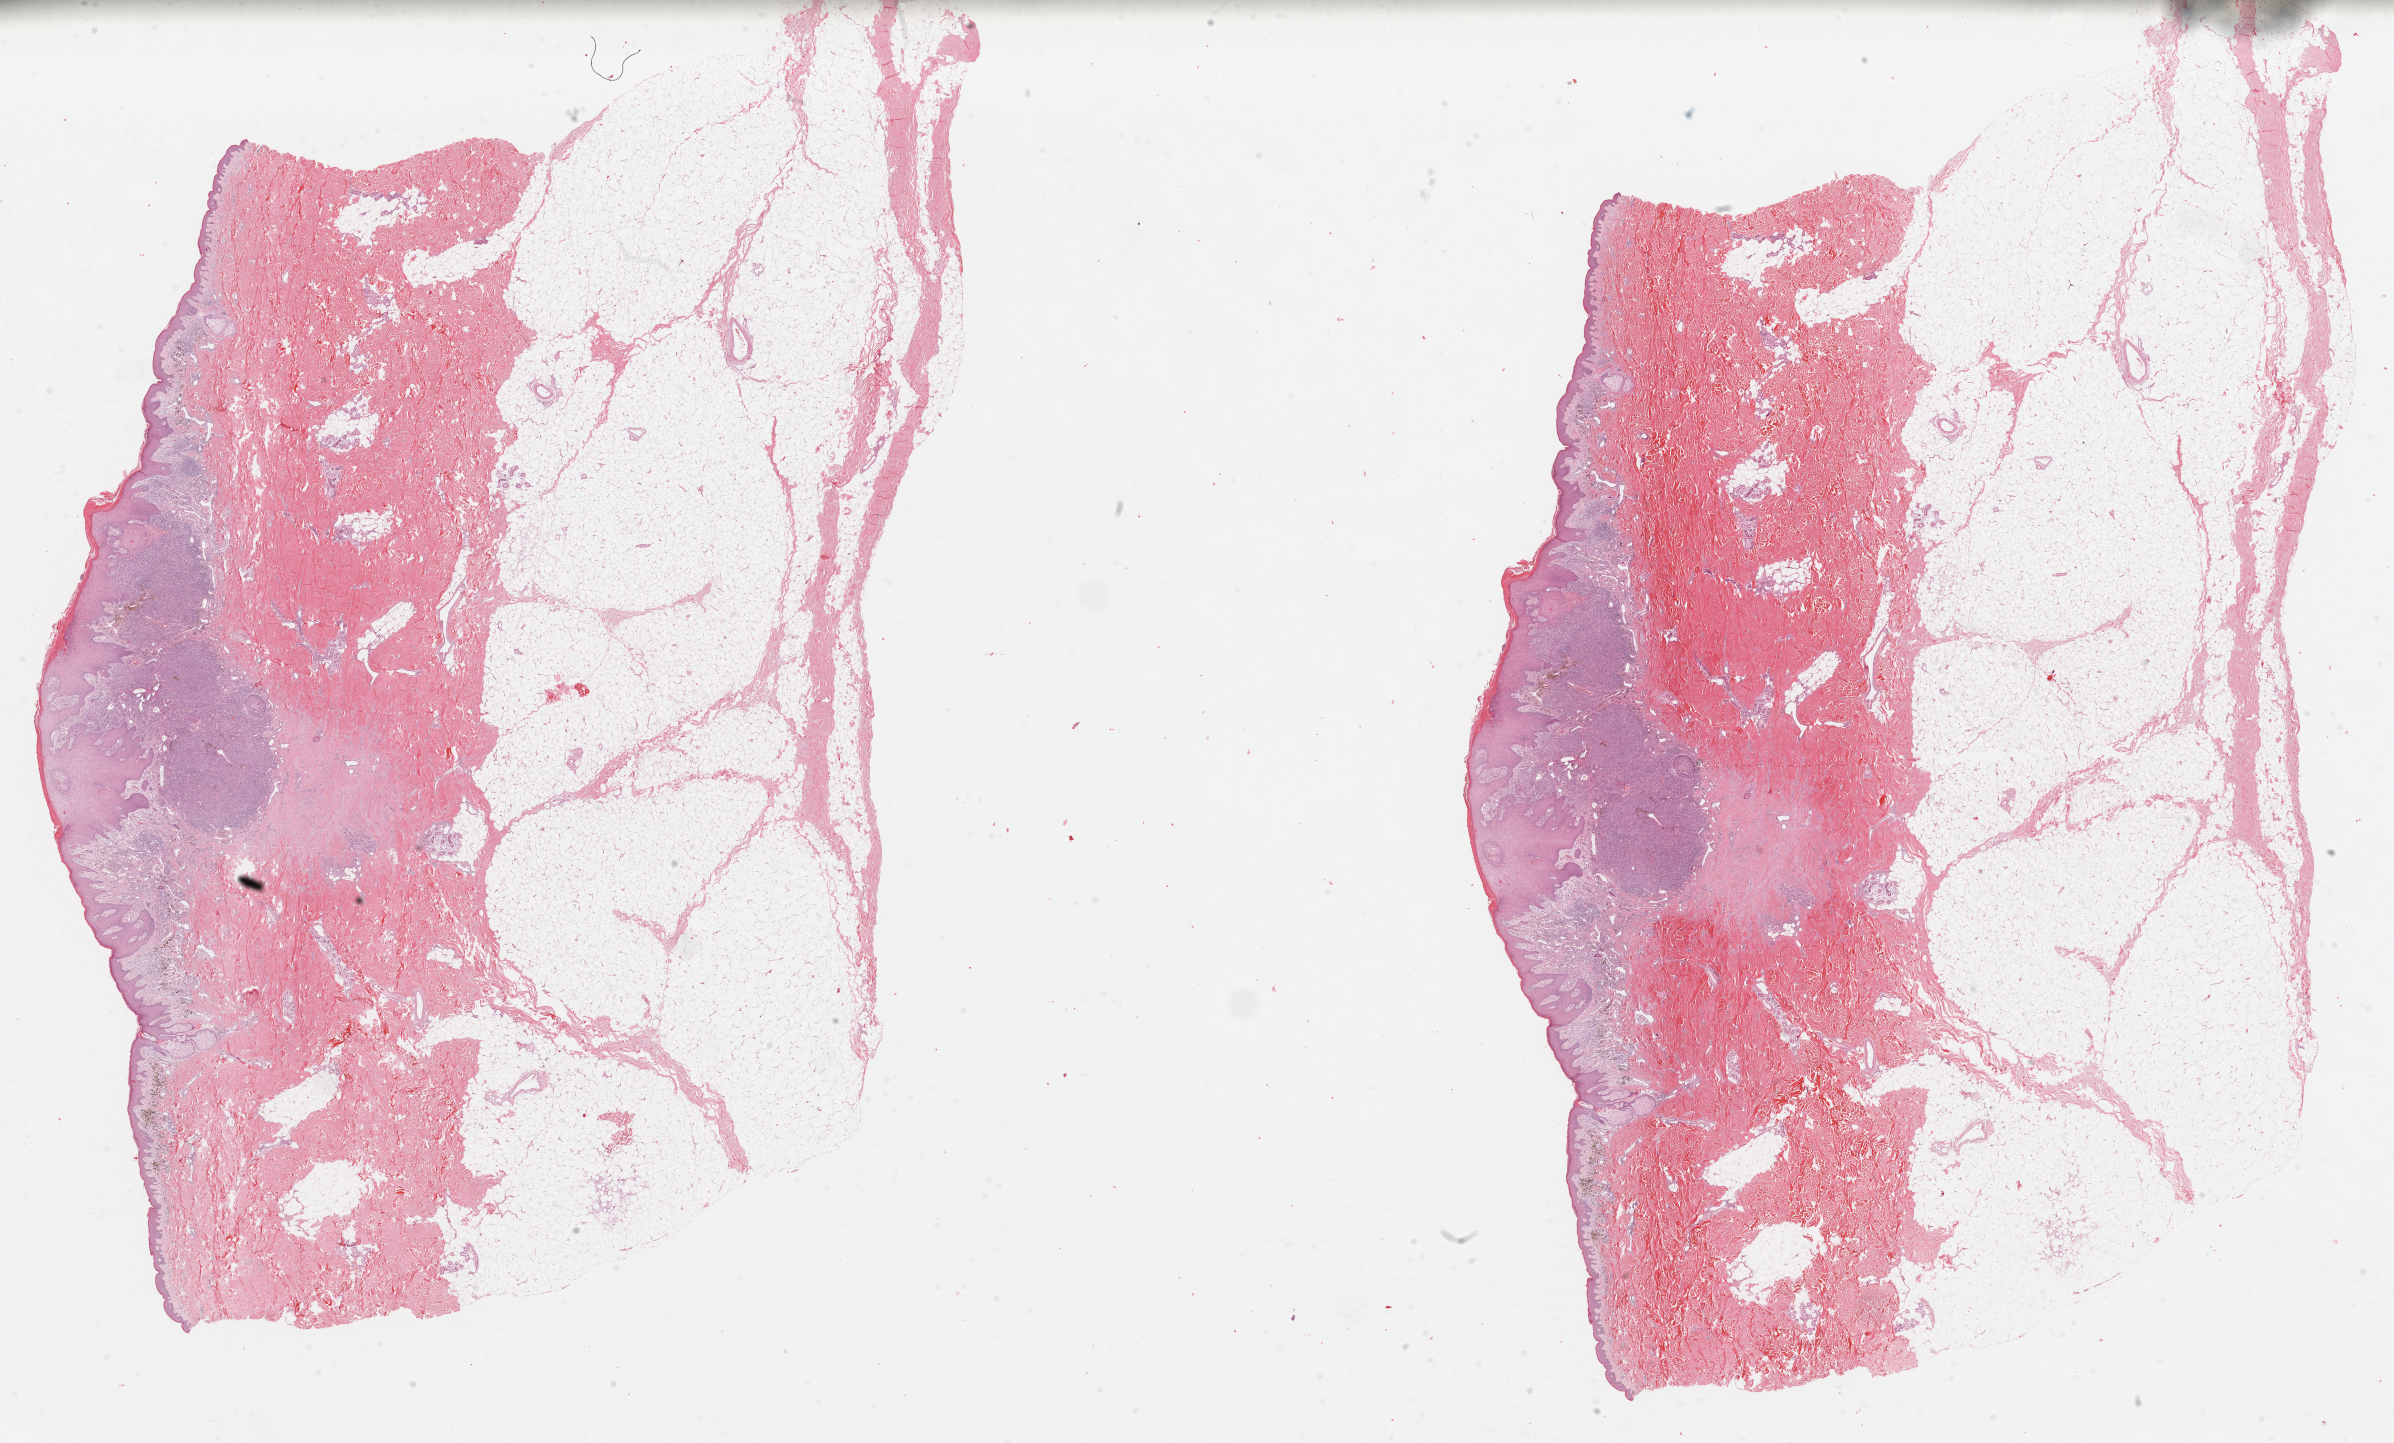
H&E whole-slide image, shown as a low-resolution overview of the whole scanned area (about 37.8 x 22.8 mm). Formalin-fixed paraffin-embedded (FFPE) diagnostic section. Primary tumour sample from the skin. Female, age 61 years at initial diagnosis.
Pathologic diagnosis: Malignant melanoma, NOS. AJCC pathologic stage: IB (7th edition).